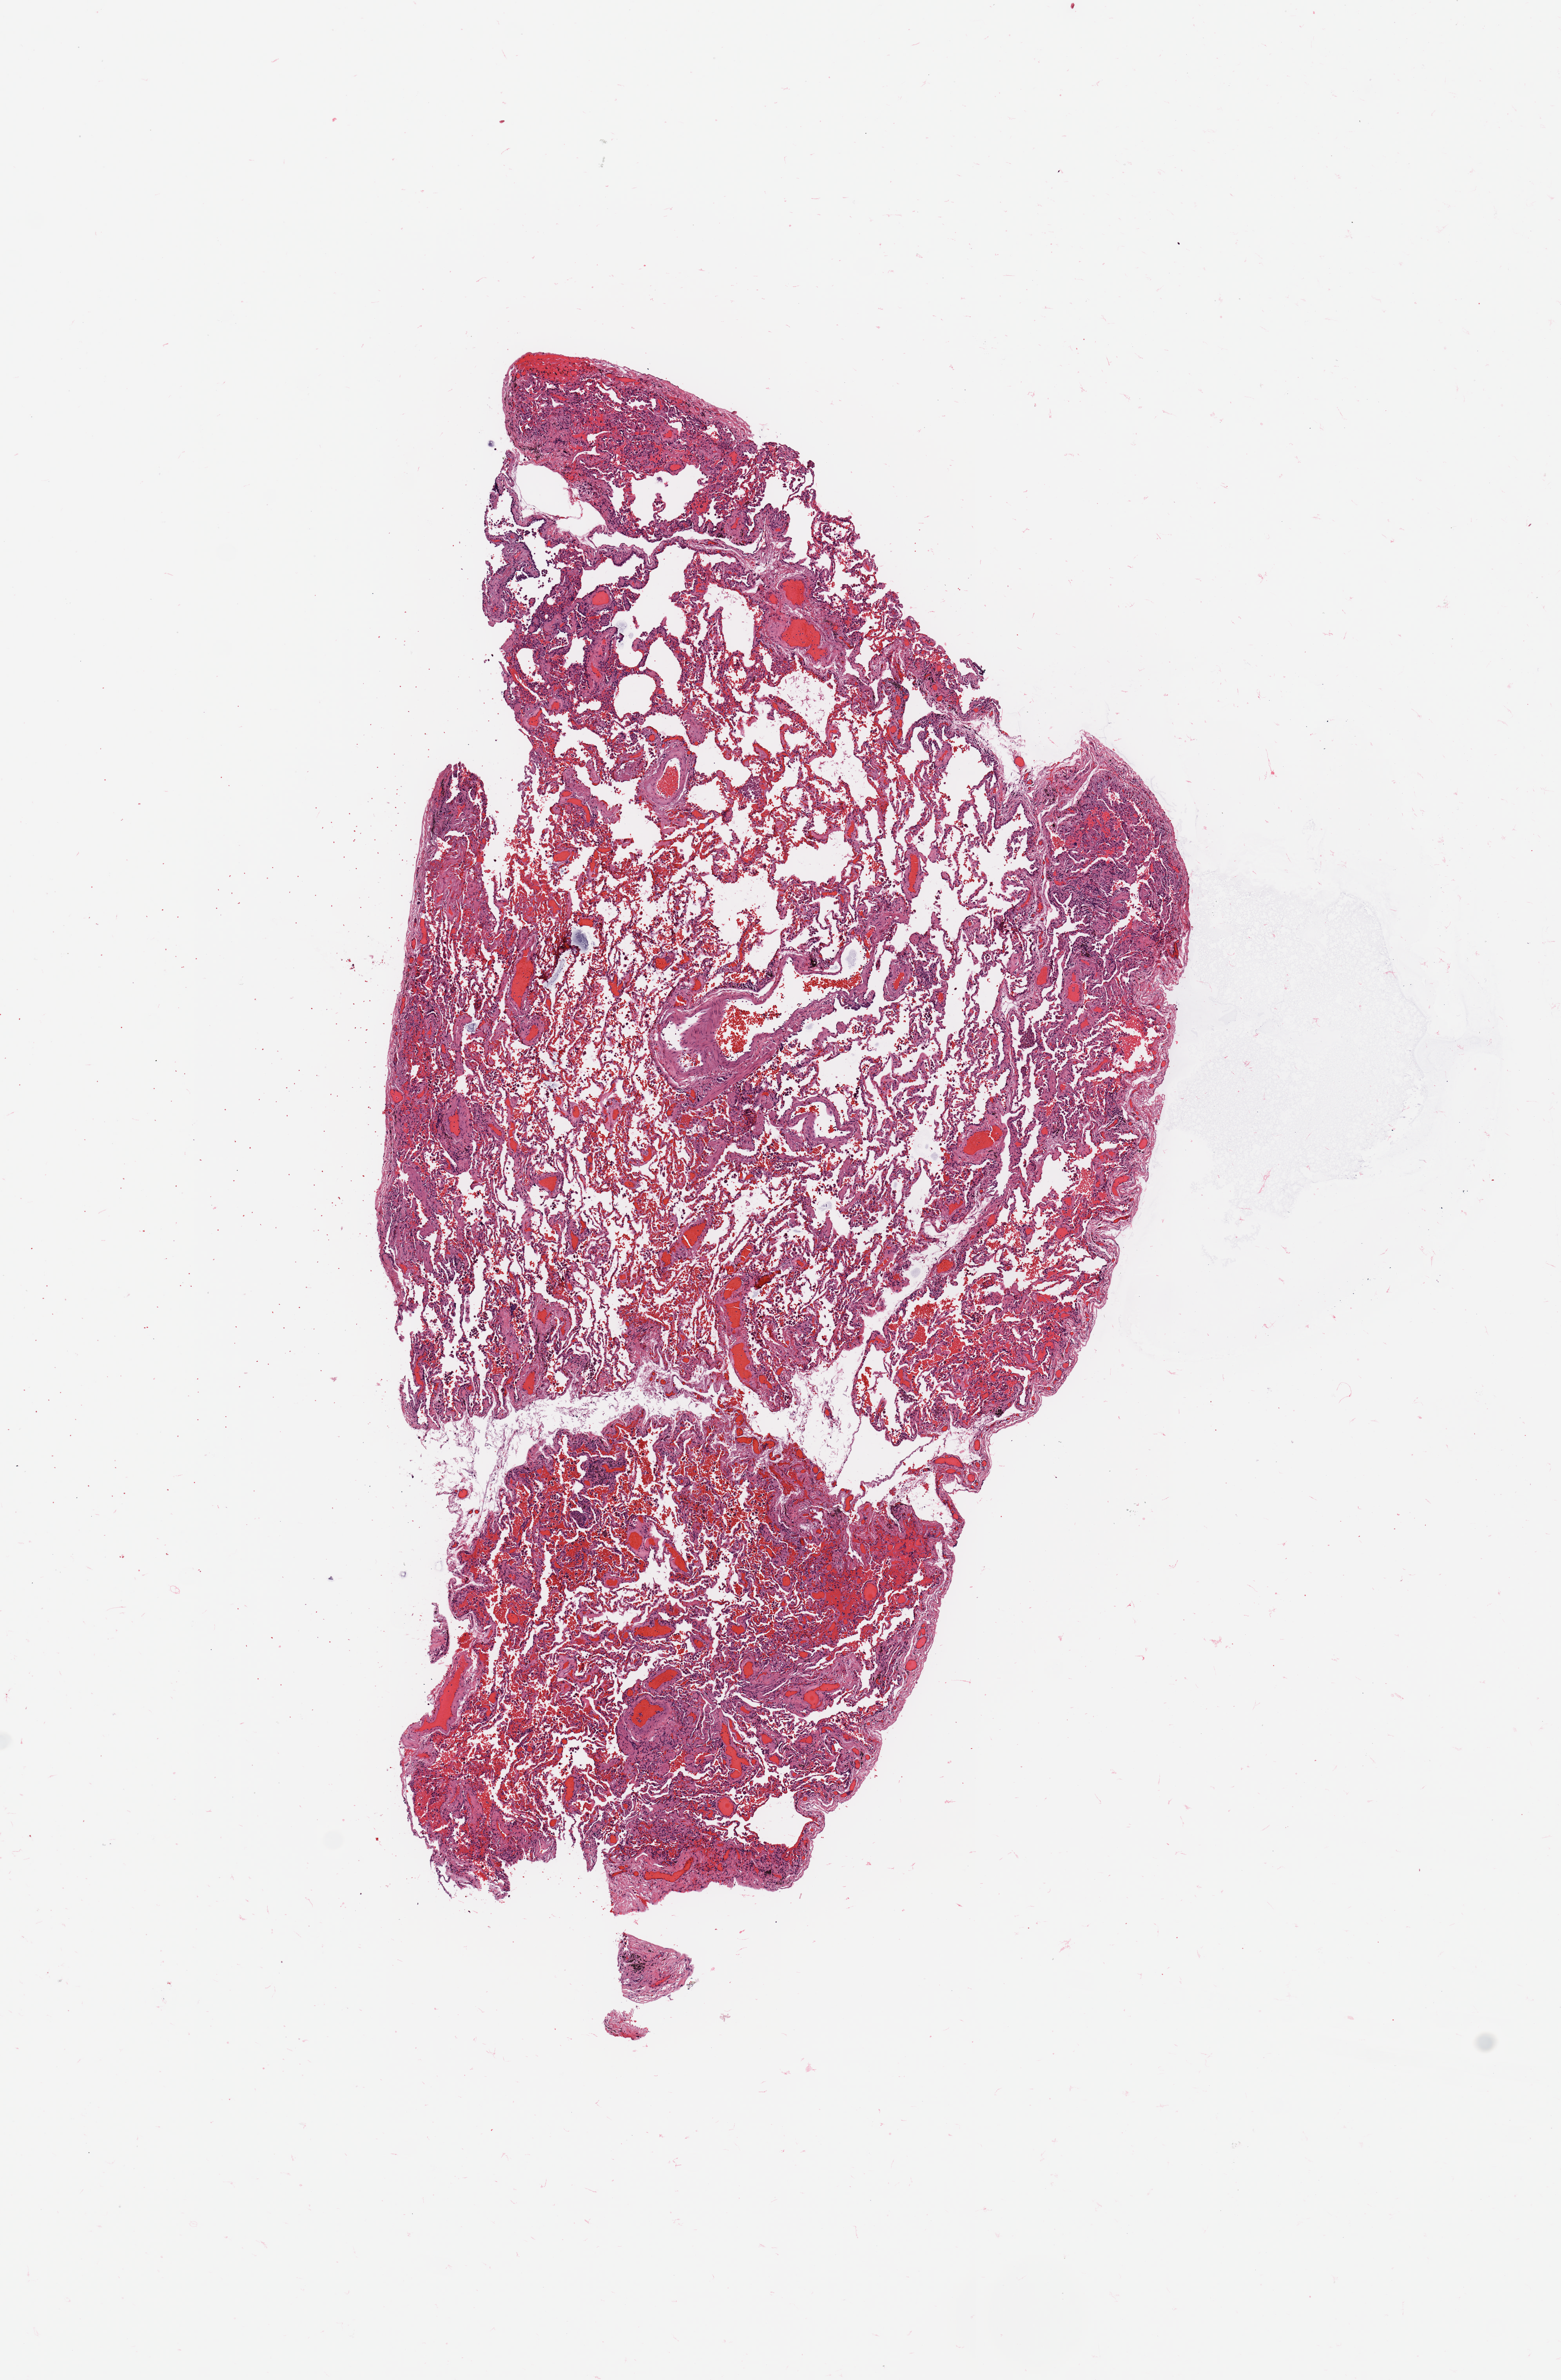
Digitized H&E-stained tissue section (whole slide), a low-resolution overview of the entire scanned area, about 7.9 x 12.0 mm, normal (non-tumour) tissue sample, lung. Patient: male, age 71 years.
This section: normal (non-tumour) tissue from the same patient. Patient diagnosis: Adenocarcinoma, NOS.